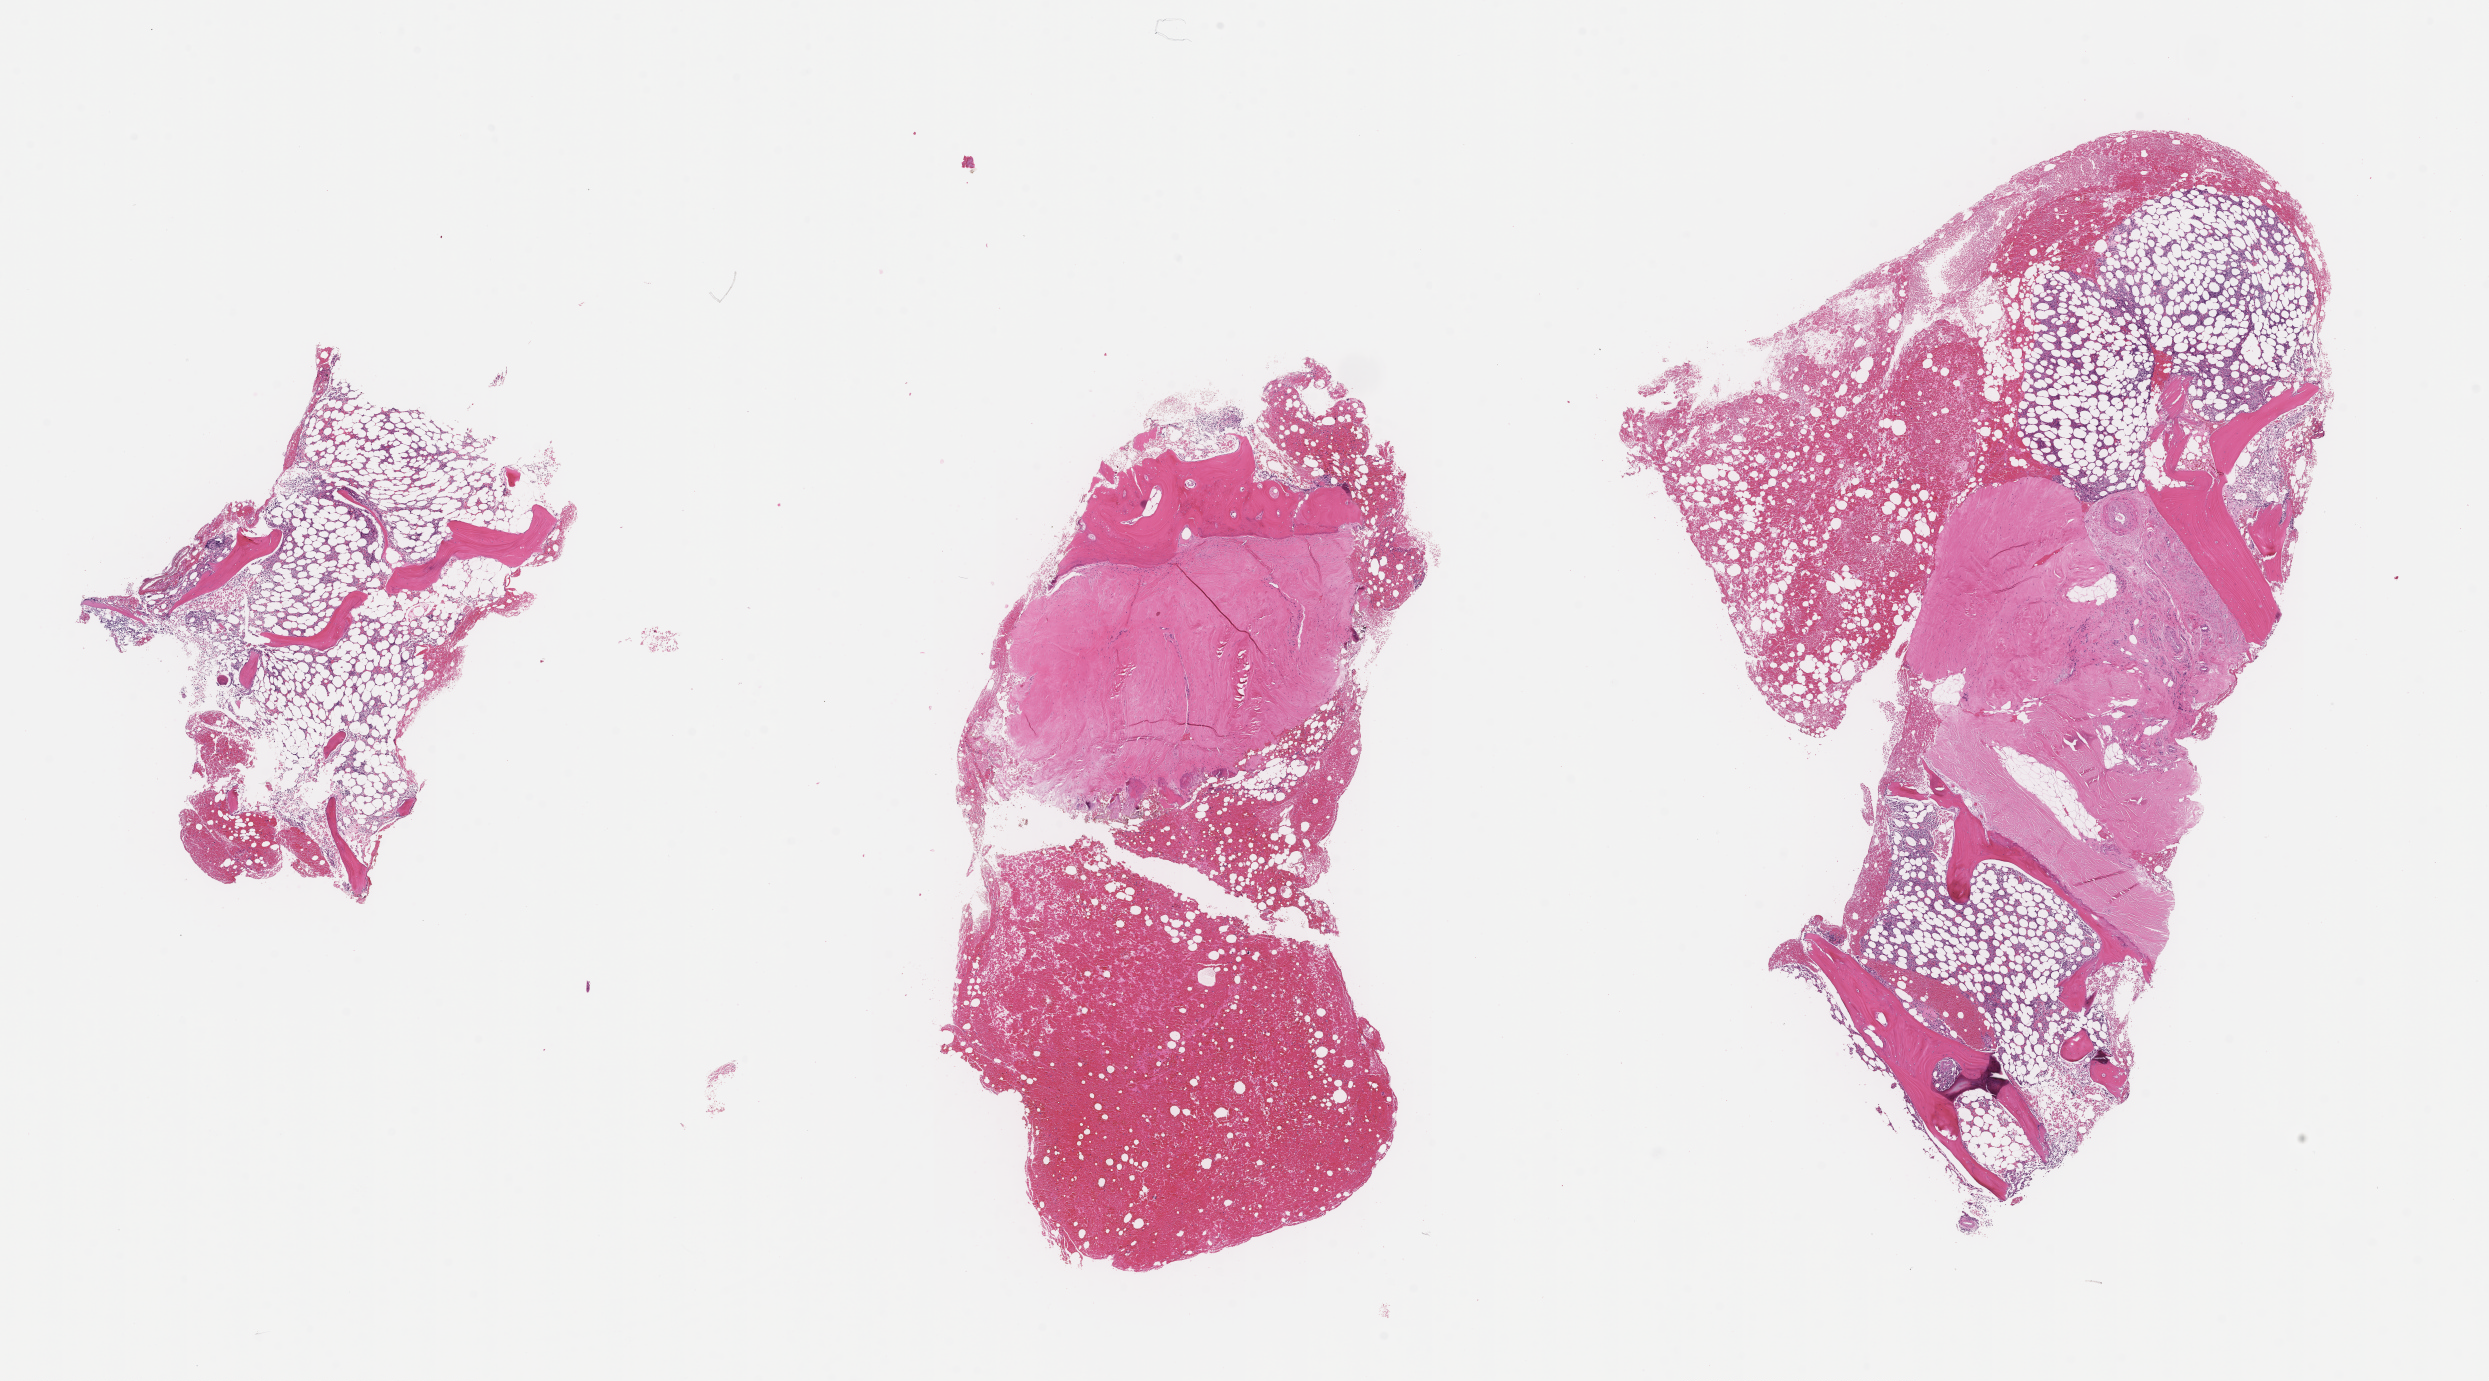
Digitized hematoxylin and eosin (H&E)-stained section — shown as a low-resolution overview of the whole scanned area (about 20.1 x 11.2 mm). Formalin-fixed paraffin-embedded section. Site: bone marrow. Specimen time point: collected at baseline (before treatment). Patient sex: male.
This section: primary tumour tissue. Diagnosis: Plasma Cell Myeloma.